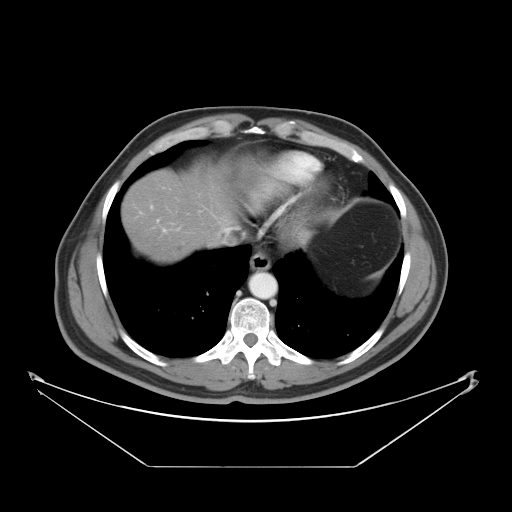
Contrast-enhanced abdominal CT, one axial slice; slice 40 of 46 in the series (ordered by position); reconstruction kernel STANDARD; 120 kVp; intravenous contrast given; soft-tissue window (W 400 / L 40 HU); 512 × 512 image matrix, field of view 465 × 465 mm. Male patient, age 57 years. Case-level facts recorded for this patient, not image findings: diagnosis: colorectal cancer liver metastases, imaged before liver resection; multiple liver metastases: no; largest metastasis: 3.3 cm; disease in both lobes: no.
Annotated regions visible in this slice (outlined manually by an expert reader):
- liver: bounding box (x1, y1, x2, y2) in pixels: (123, 171, 233, 262)
- planned liver remnant (the part of the liver to remain after resection): (123, 171, 233, 261)